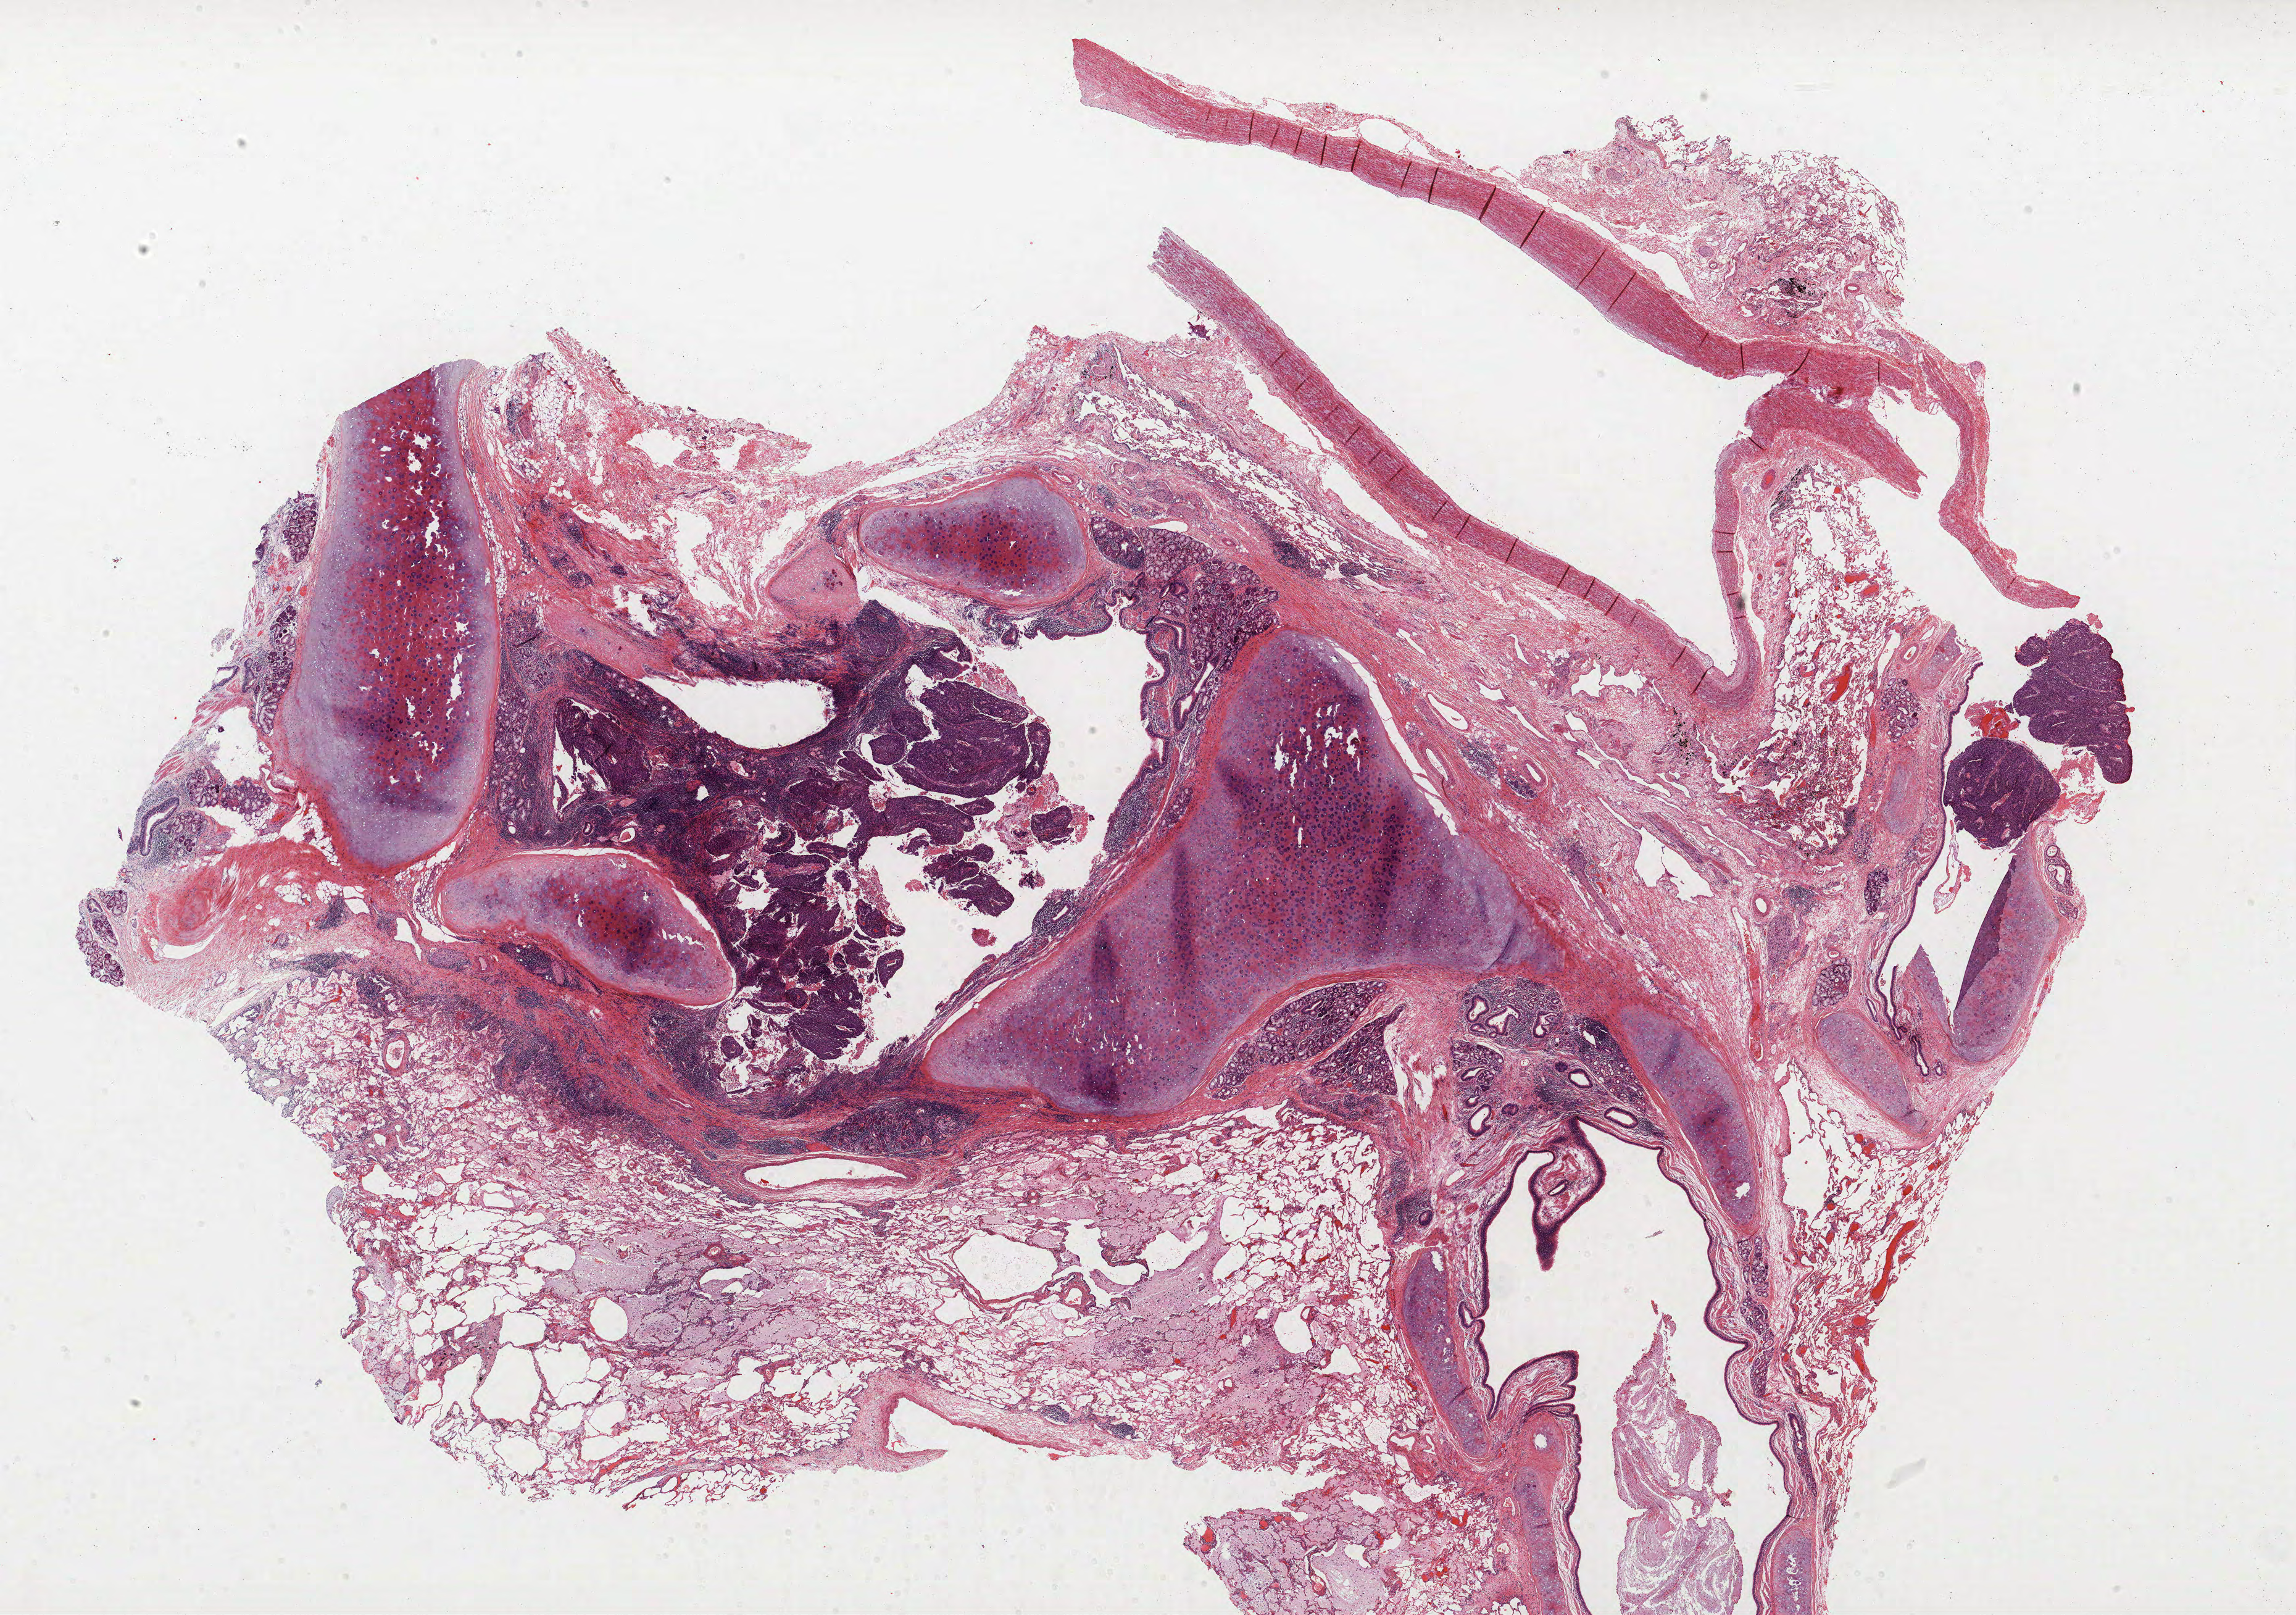
H&E-stained whole-slide image — whole scanned area (about 29.8 x 20.9 mm) shown as a low-resolution overview, formalin-fixed paraffin-embedded (FFPE) section, lung tissue. Male, age 57 at enrolment. Former smoker at enrolment.
- tumour size (pathology): 15 mm
- participant's lung-cancer diagnosis: Squamous cell carcinoma, NOS (ICD-O-3 8070/3)
- stage (AJCC 6th edition): IA
- primary tumour location (clinical record): right upper lobe